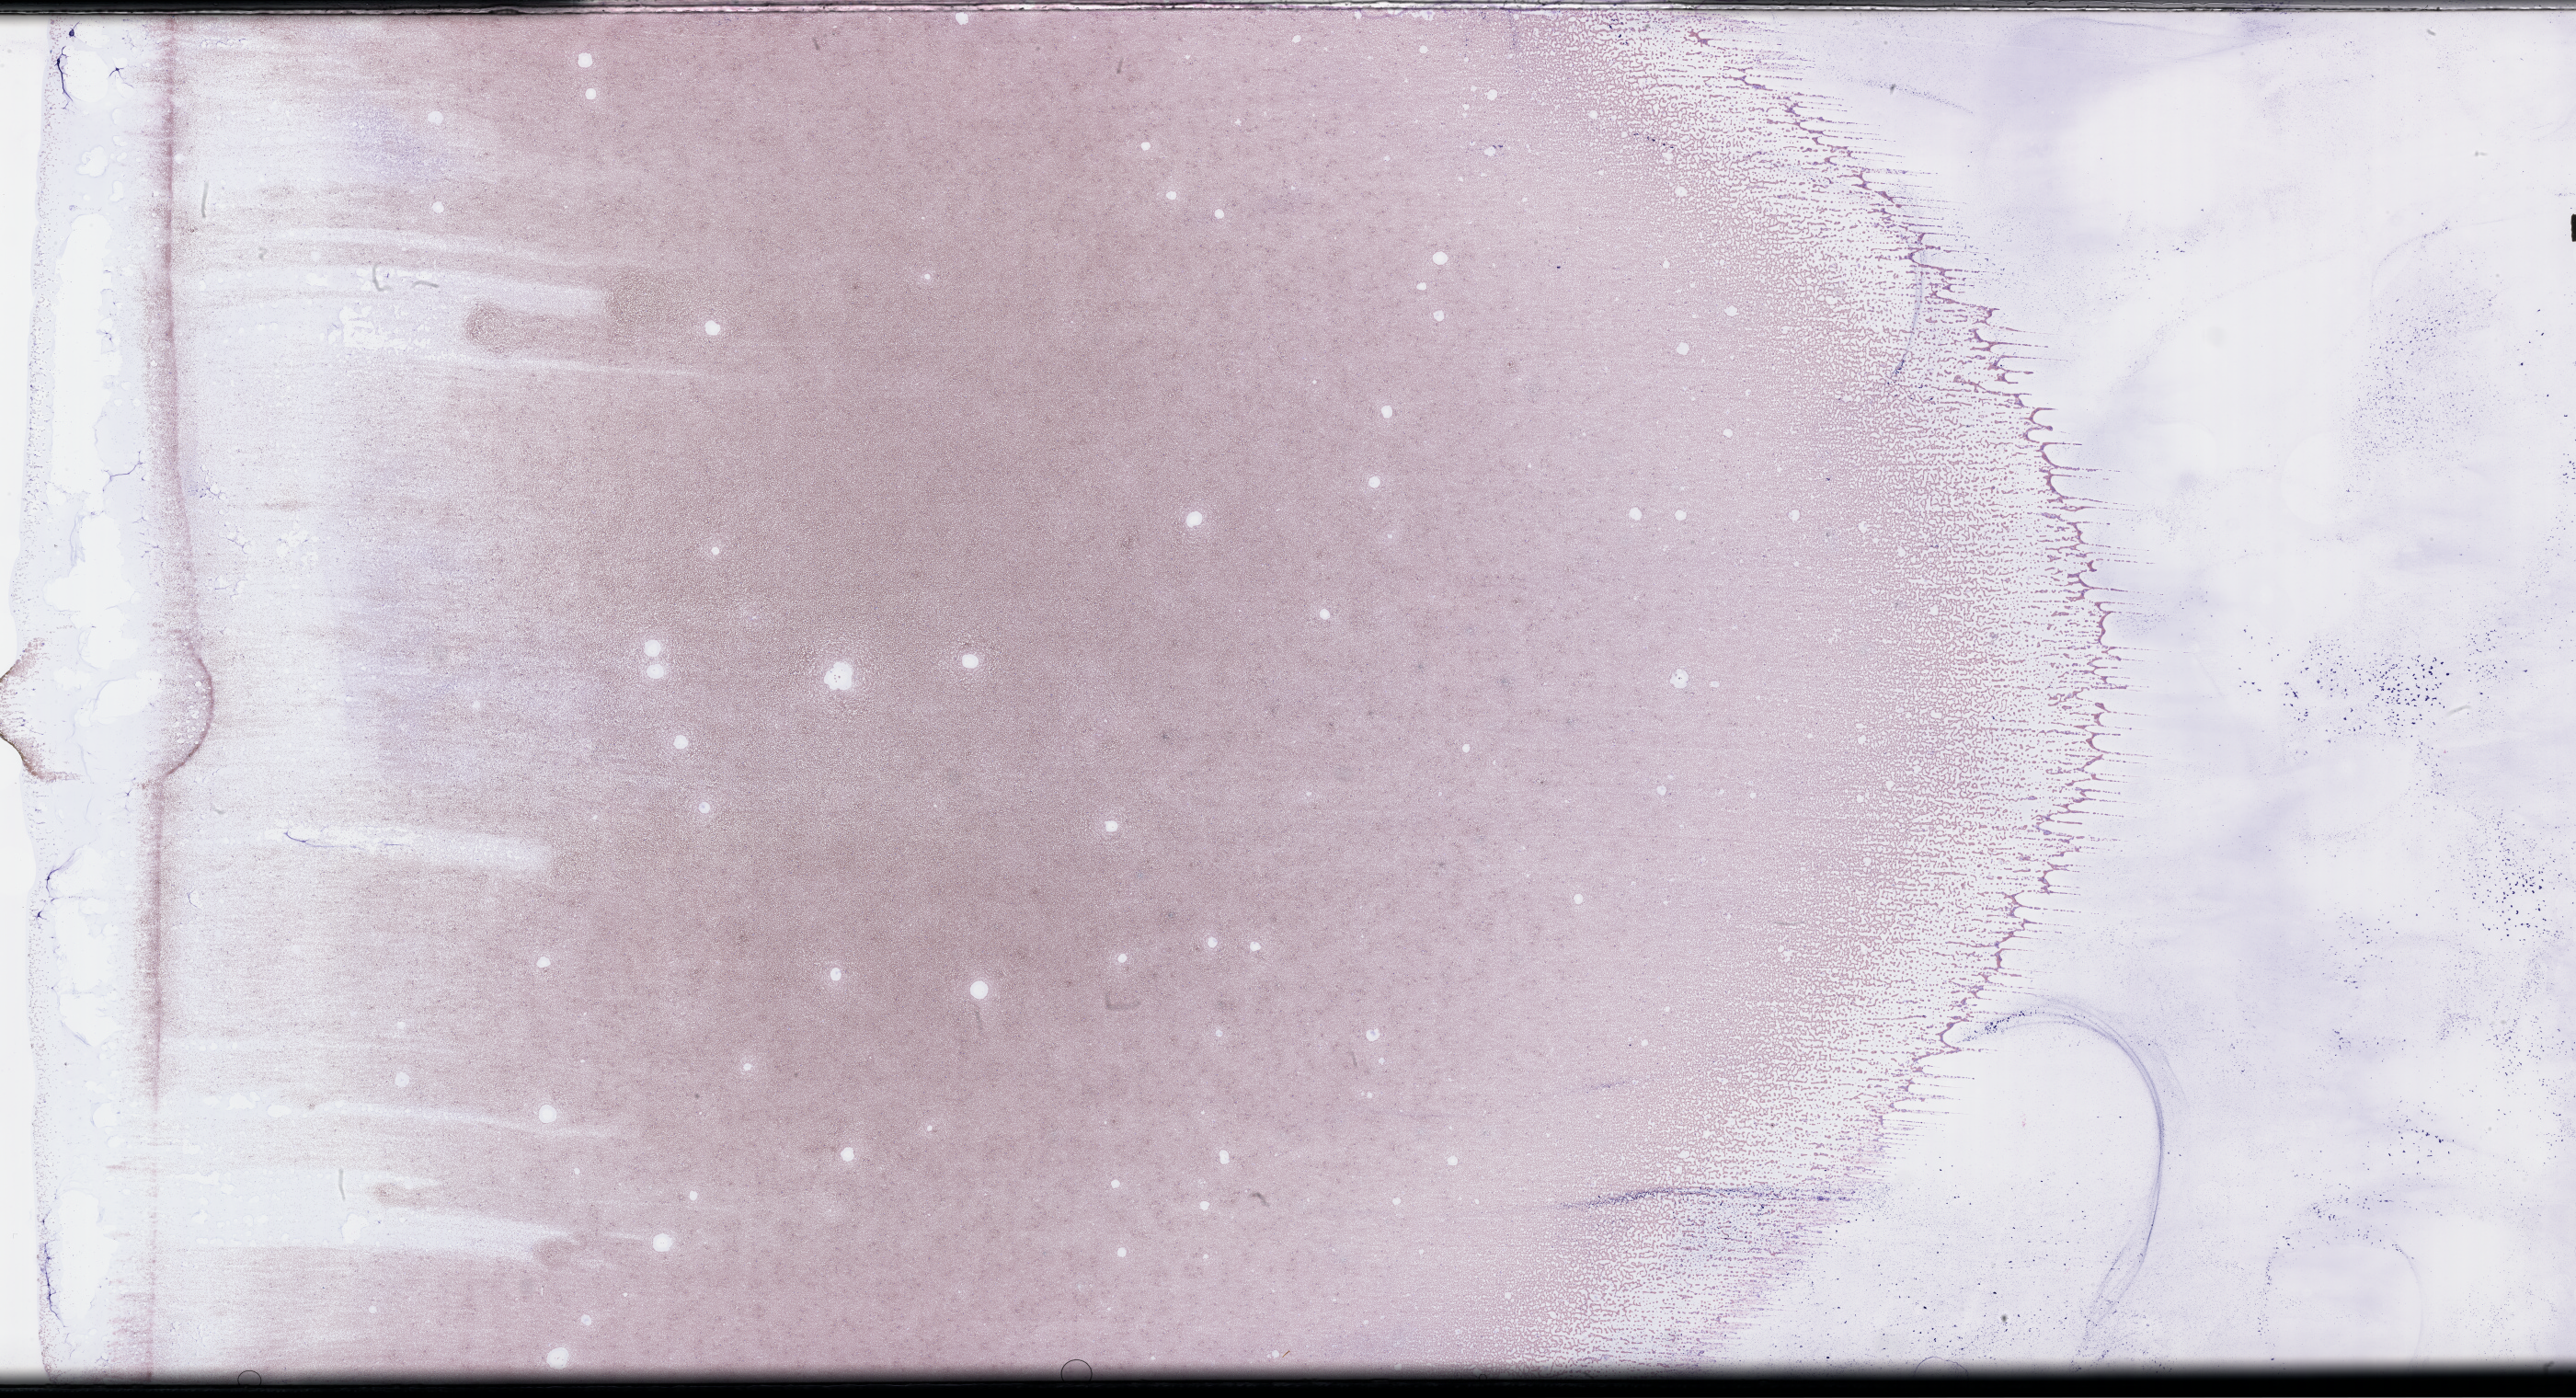
Whole-slide image of a bone marrow smear, Wright-Giemsa stain, shown as a low-resolution overview of the whole scanned area (about 45.2 x 24.5 mm); EDTA-anticoagulated smear; specimen time point: collected post-treatment, no progression. Patient sex: female.
Patient diagnosis: Acute Myeloid Leukemia Not Otherwise Specified.